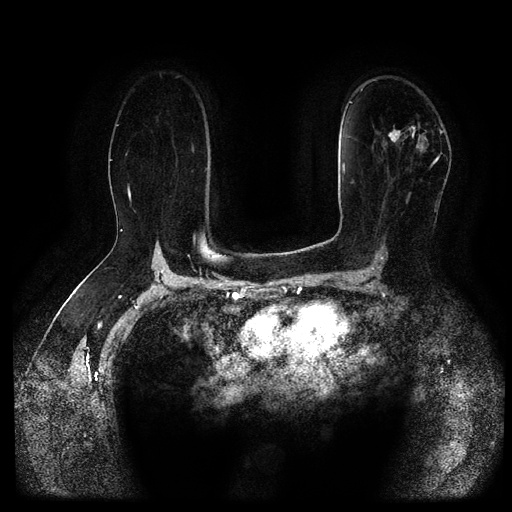
Breast MRI (dynamic contrast-enhanced, multi-phase), one axial slice. Position 67 of 116 along the scan axis. Dynamic contrast-enhanced series, time point 2 of 5 at this slice position (early post-contrast). 1.5 T. TE 2.6 ms, TR 5.3 ms. 512 × 512 image matrix, field of view 360 × 360 mm. Female patient, age 67 years.
Structures marked on this image (semi-automatically segmented with operator editing):
- breast lesion (labelled 'tumour' in the annotation; benign lesions carry a separate 'benign' label): bounding box [x1, y1, x2, y2] px = [388, 123, 419, 148]